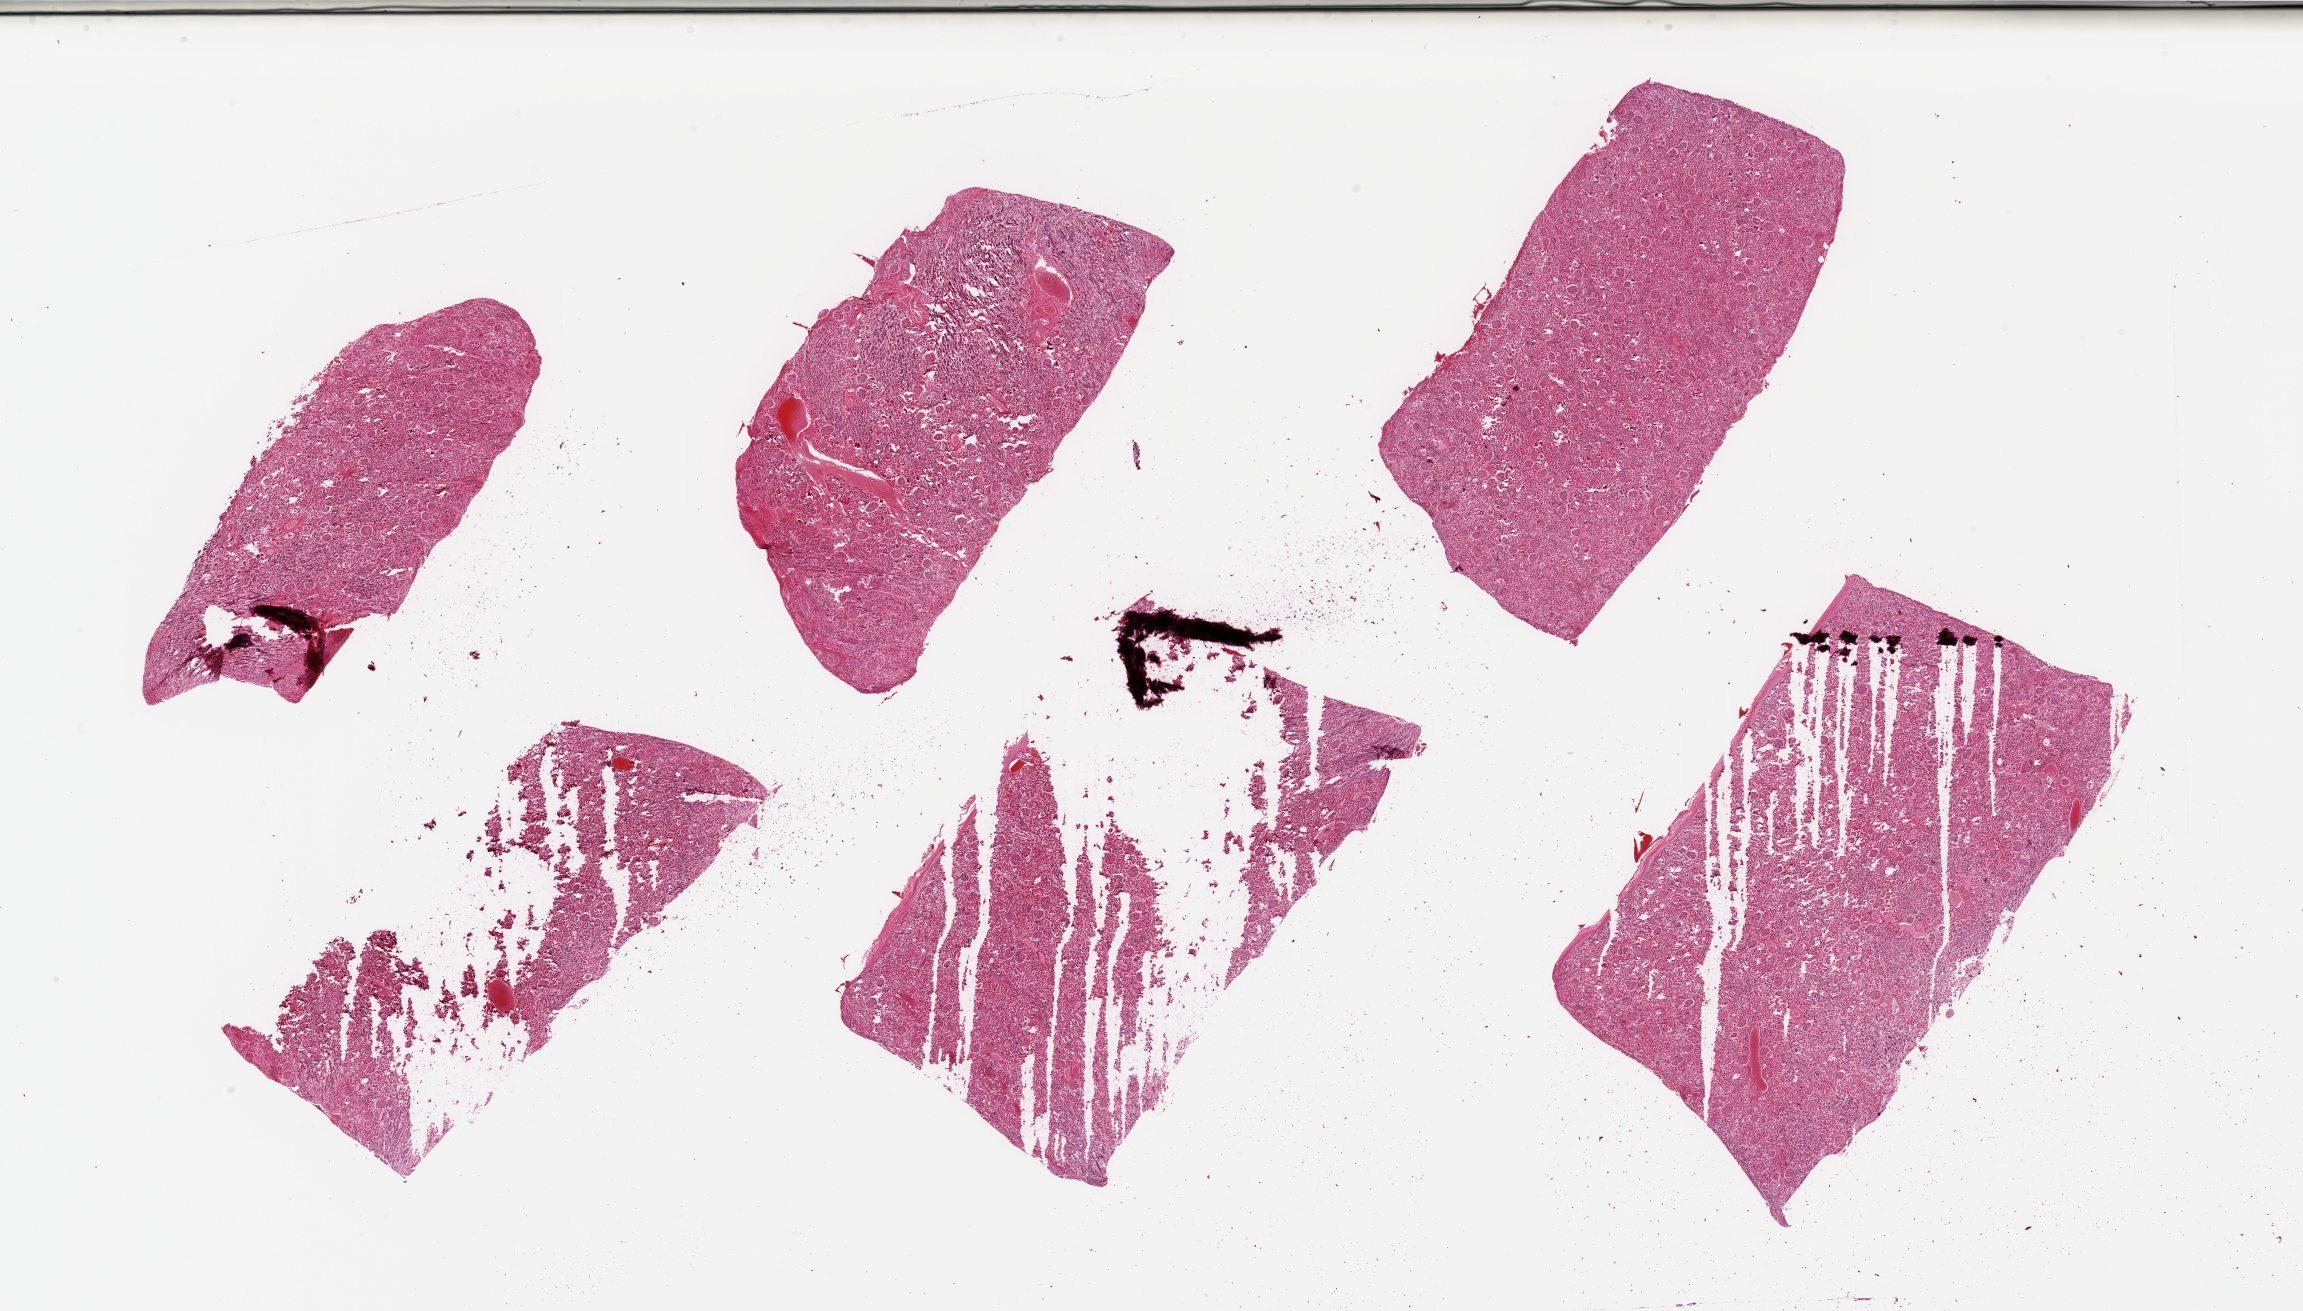
Digitized hematoxylin and eosin (H&E)-stained section, brightfield, a low-resolution overview of the entire scanned area, about 36.4 x 20.7 mm; PAXgene-fixed paraffin-embedded (PFPE) section; sampled site (target tissue): renal cortex; donor tissue sample. Male donor.
Review note (as recorded): 6 pieces; 3 pieces extensively fragmented; no sign of glomerular, vascular or tubular lesions.